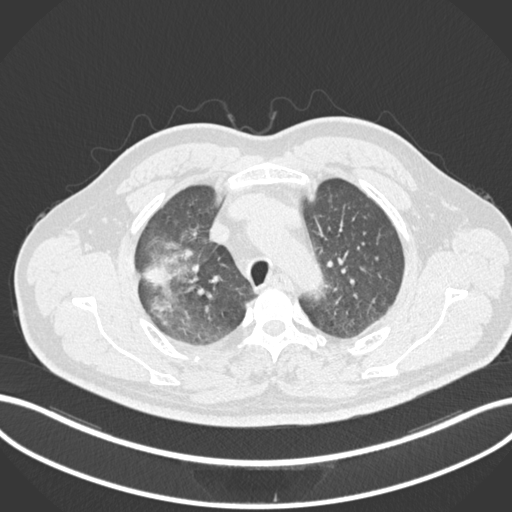
Chest CT, one axial slice; slice 681 of 852 in the series (ordered by position); 120 kVp; lung window (W 1500 / L -600 HU); 512 × 512 image matrix, field of view 400 × 400 mm. Male patient, age 55 years. From the clinical record (not read from this slice): clinical TNM (as recorded): T3 N2 M1.
Outlined on this slice (bounding box drawn by a radiologist):
- lung tumour (recorded histology: adenocarcinoma): bounding box (x1, y1, x2, y2) in pixels: (140, 262, 175, 285)